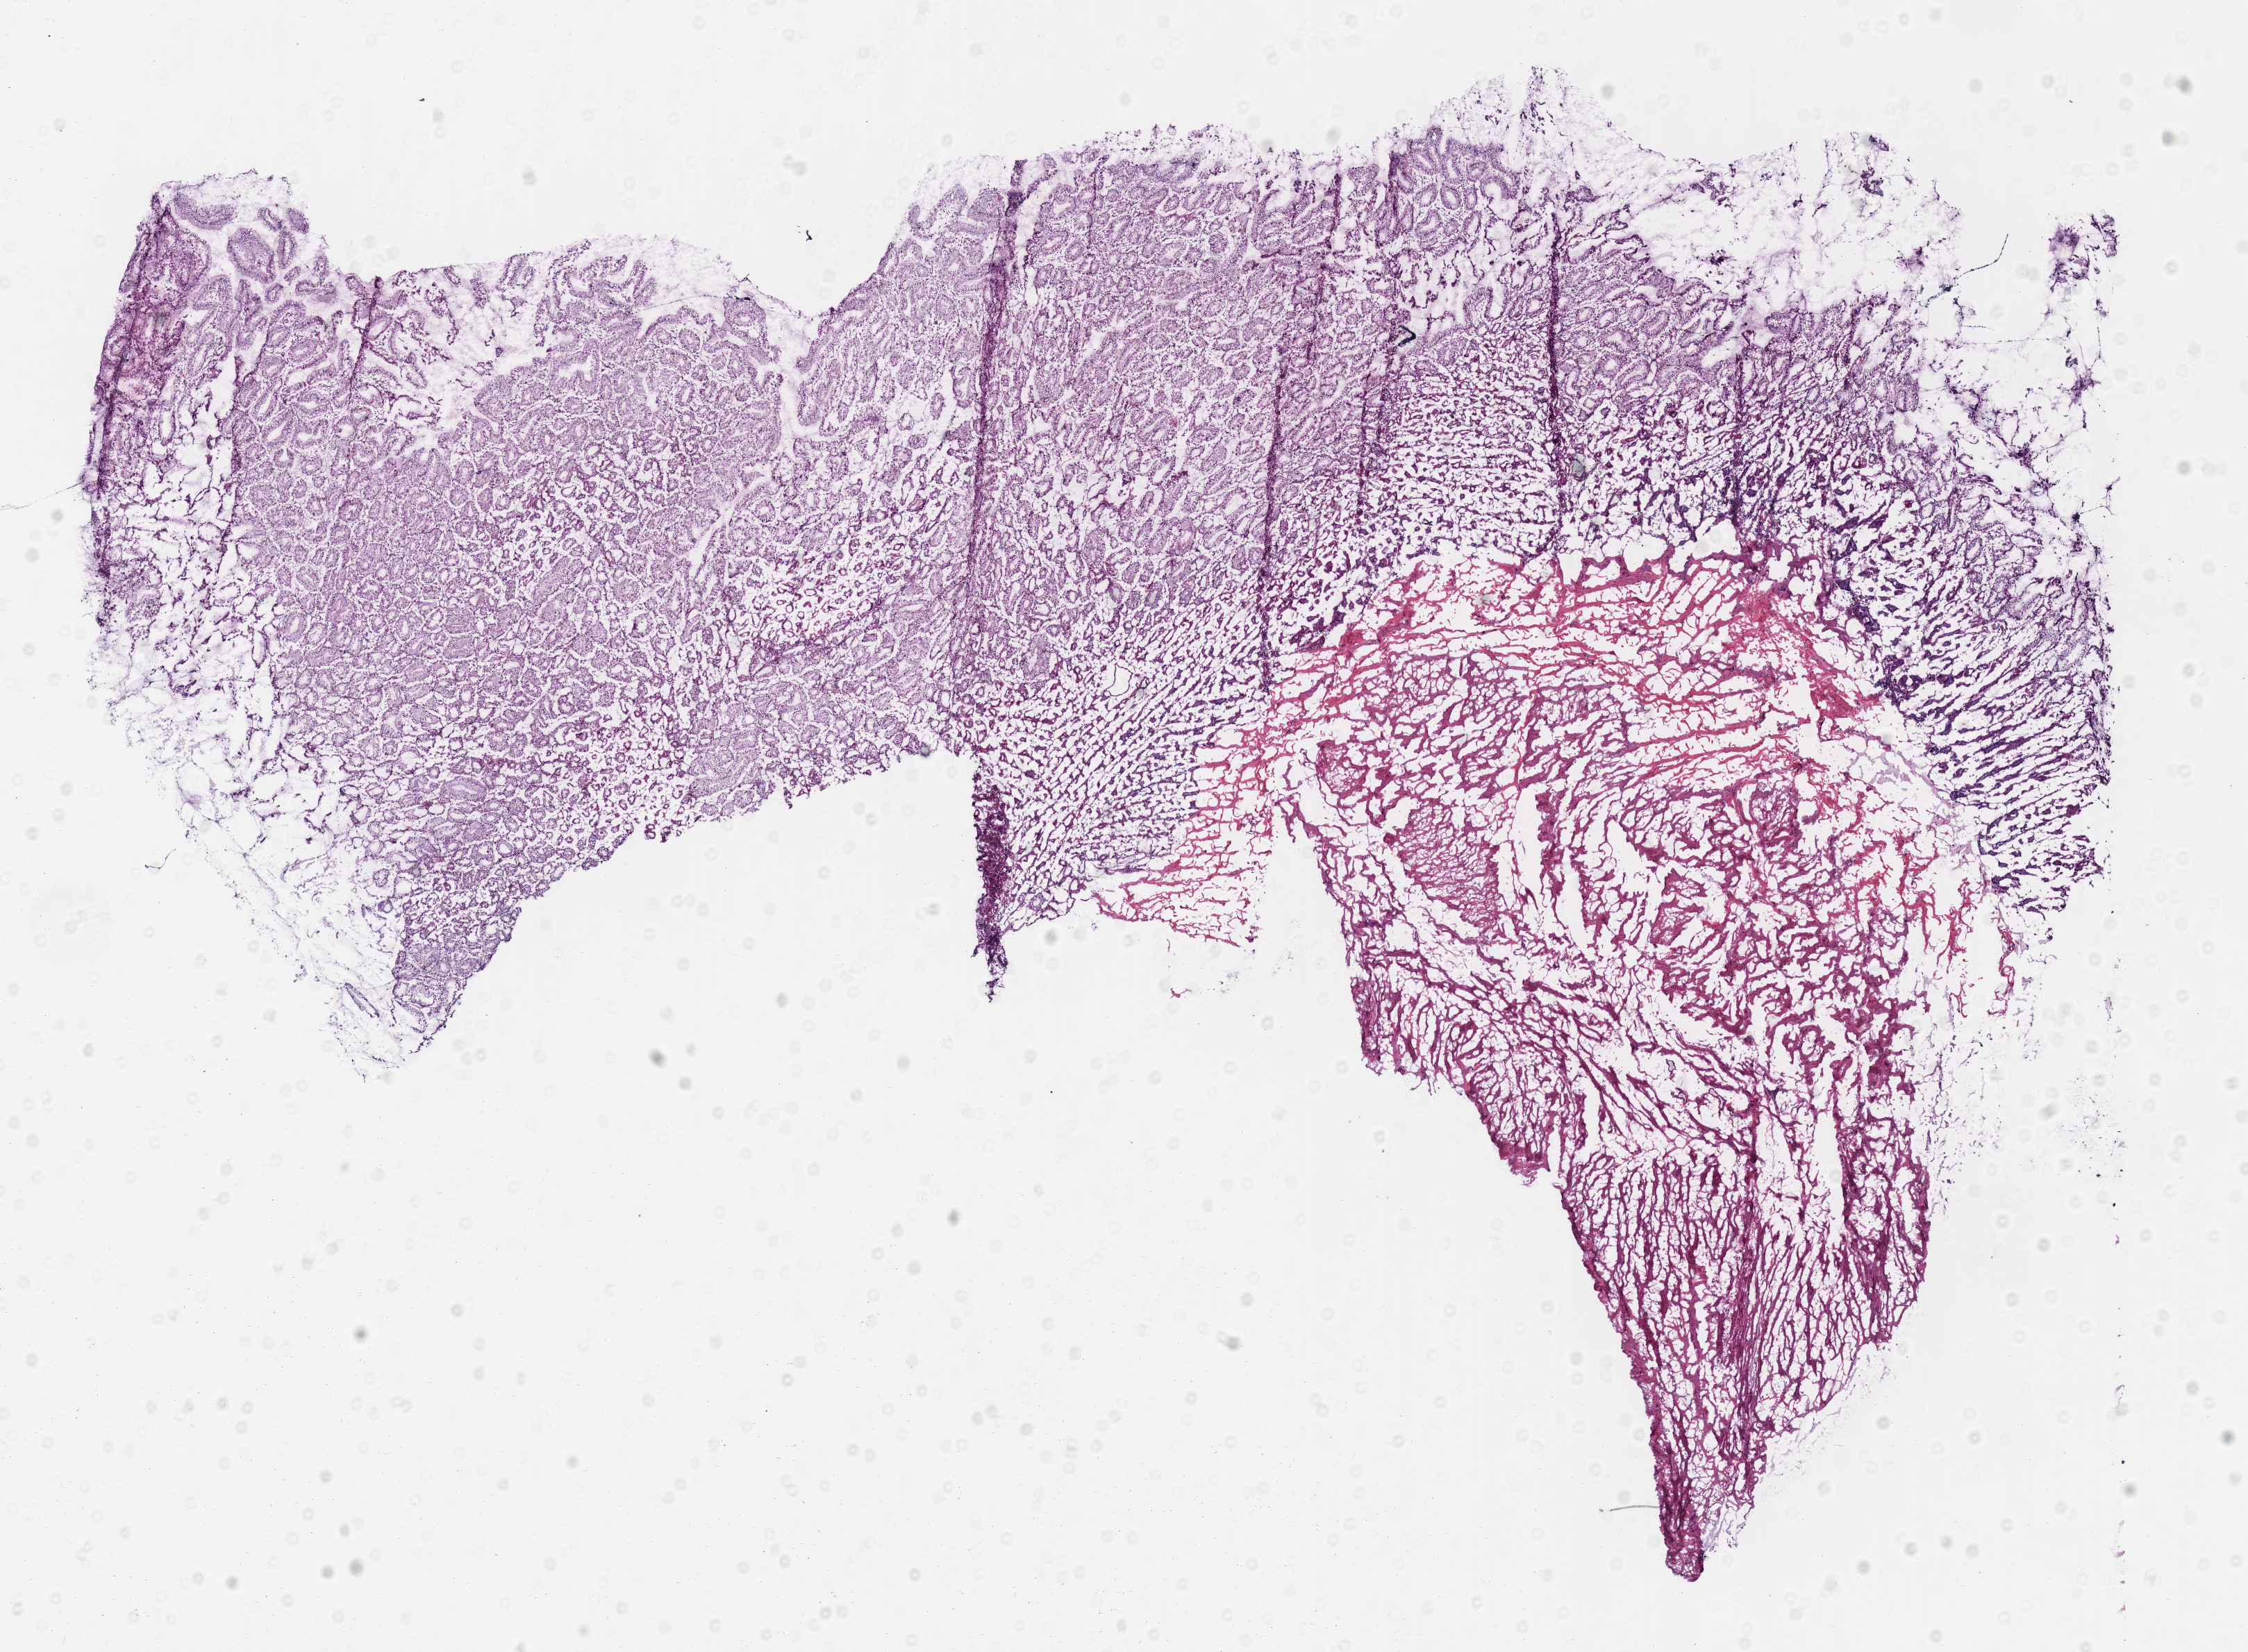
H&E-stained whole-slide image — a low-resolution overview of the entire scanned area, about 12.7 x 9.4 mm, frozen section from the top of the tissue portion, solid tissue normal (non-tumour tissue) sample from the stomach. Female, age 75 years at initial diagnosis. Inflammatory infiltration, as recorded: lymphocyte infiltration 8%, monocyte infiltration 2%.
This section: solid tissue normal sample (biorepository sample class). Patient diagnosis: Adenocarcinoma, NOS.